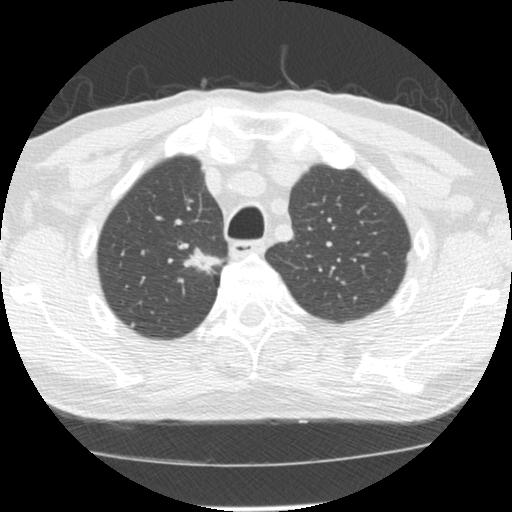
Chest CT (low-dose screening protocol), one axial image; first (baseline) screen; lung window (W 1500 / L -600 HU); standard (soft-tissue) reconstruction kernel (STANDARD). Male participant, aged 64 years at enrolment. Former smoker at enrolment.
Expert-annotated lung lesion, bounding box (x1, y1, x2, y2) in pixels: (174, 236, 224, 278). The exam's reader record, not a measurement of the box and not confirmed to be the same lesion: non-calcified nodule or mass ≥4 mm, right upper lobe, 20 × 13 mm, spiculated (stellate) margins, soft tissue attenuation. Participant outcome: lung cancer diagnosed 73 days after this screen — adenocarcinoma, NOS, right upper lobe, moderately differentiated (G2), stage IA (AJCC 6th edition), 17 mm at pathology.